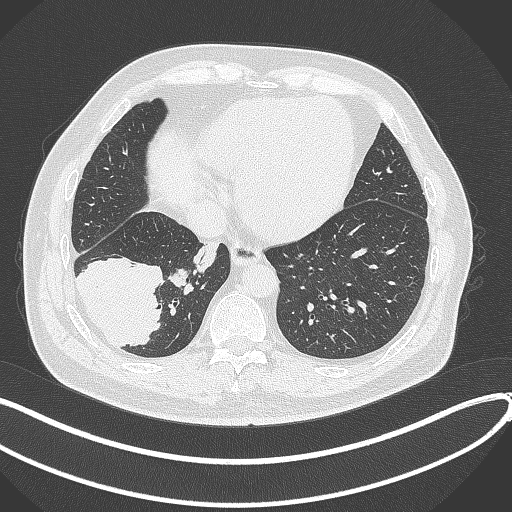
Chest CT, one axial slice; slice 99 of 360 in the series (ordered by position); reconstruction kernel B70f; lung window (W 1500 / L -600 HU); 1 mm slice thickness; 512 × 512 image matrix, field of view 400 × 400 mm. Male patient, age 59 years.
Structures marked on this image (bounding box drawn by a radiologist):
- lung tumour (recorded histology: adenocarcinoma): box from (x=73, y=253) to (x=167, y=351) px